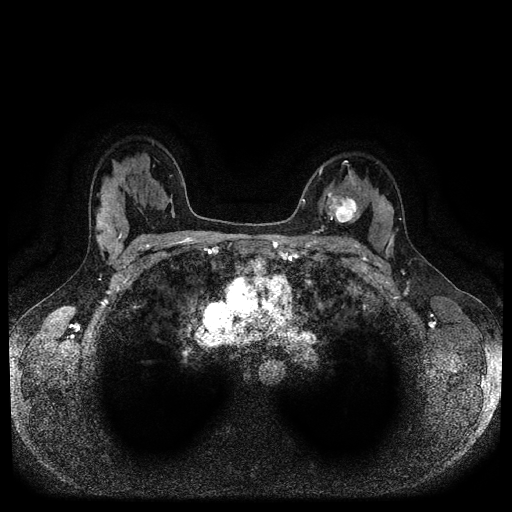
Breast MRI (dynamic contrast-enhanced, multi-phase), one axial slice; position 69 of 116 along the scan axis; dynamic contrast-enhanced series, time point 2 of 5 at this slice position (early post-contrast); 1.5 T; TE 2.6 ms, TR 5.3 ms; 2 mm slice thickness; 512 × 512 image matrix, field of view 350 × 350 mm. Patient: female, 33 years.
Structures marked on this image (semi-automatically segmented with operator editing):
- breast lesion (labelled 'tumour' in the annotation; benign lesions carry a separate 'benign' label): box from (x=324, y=189) to (x=357, y=223) px